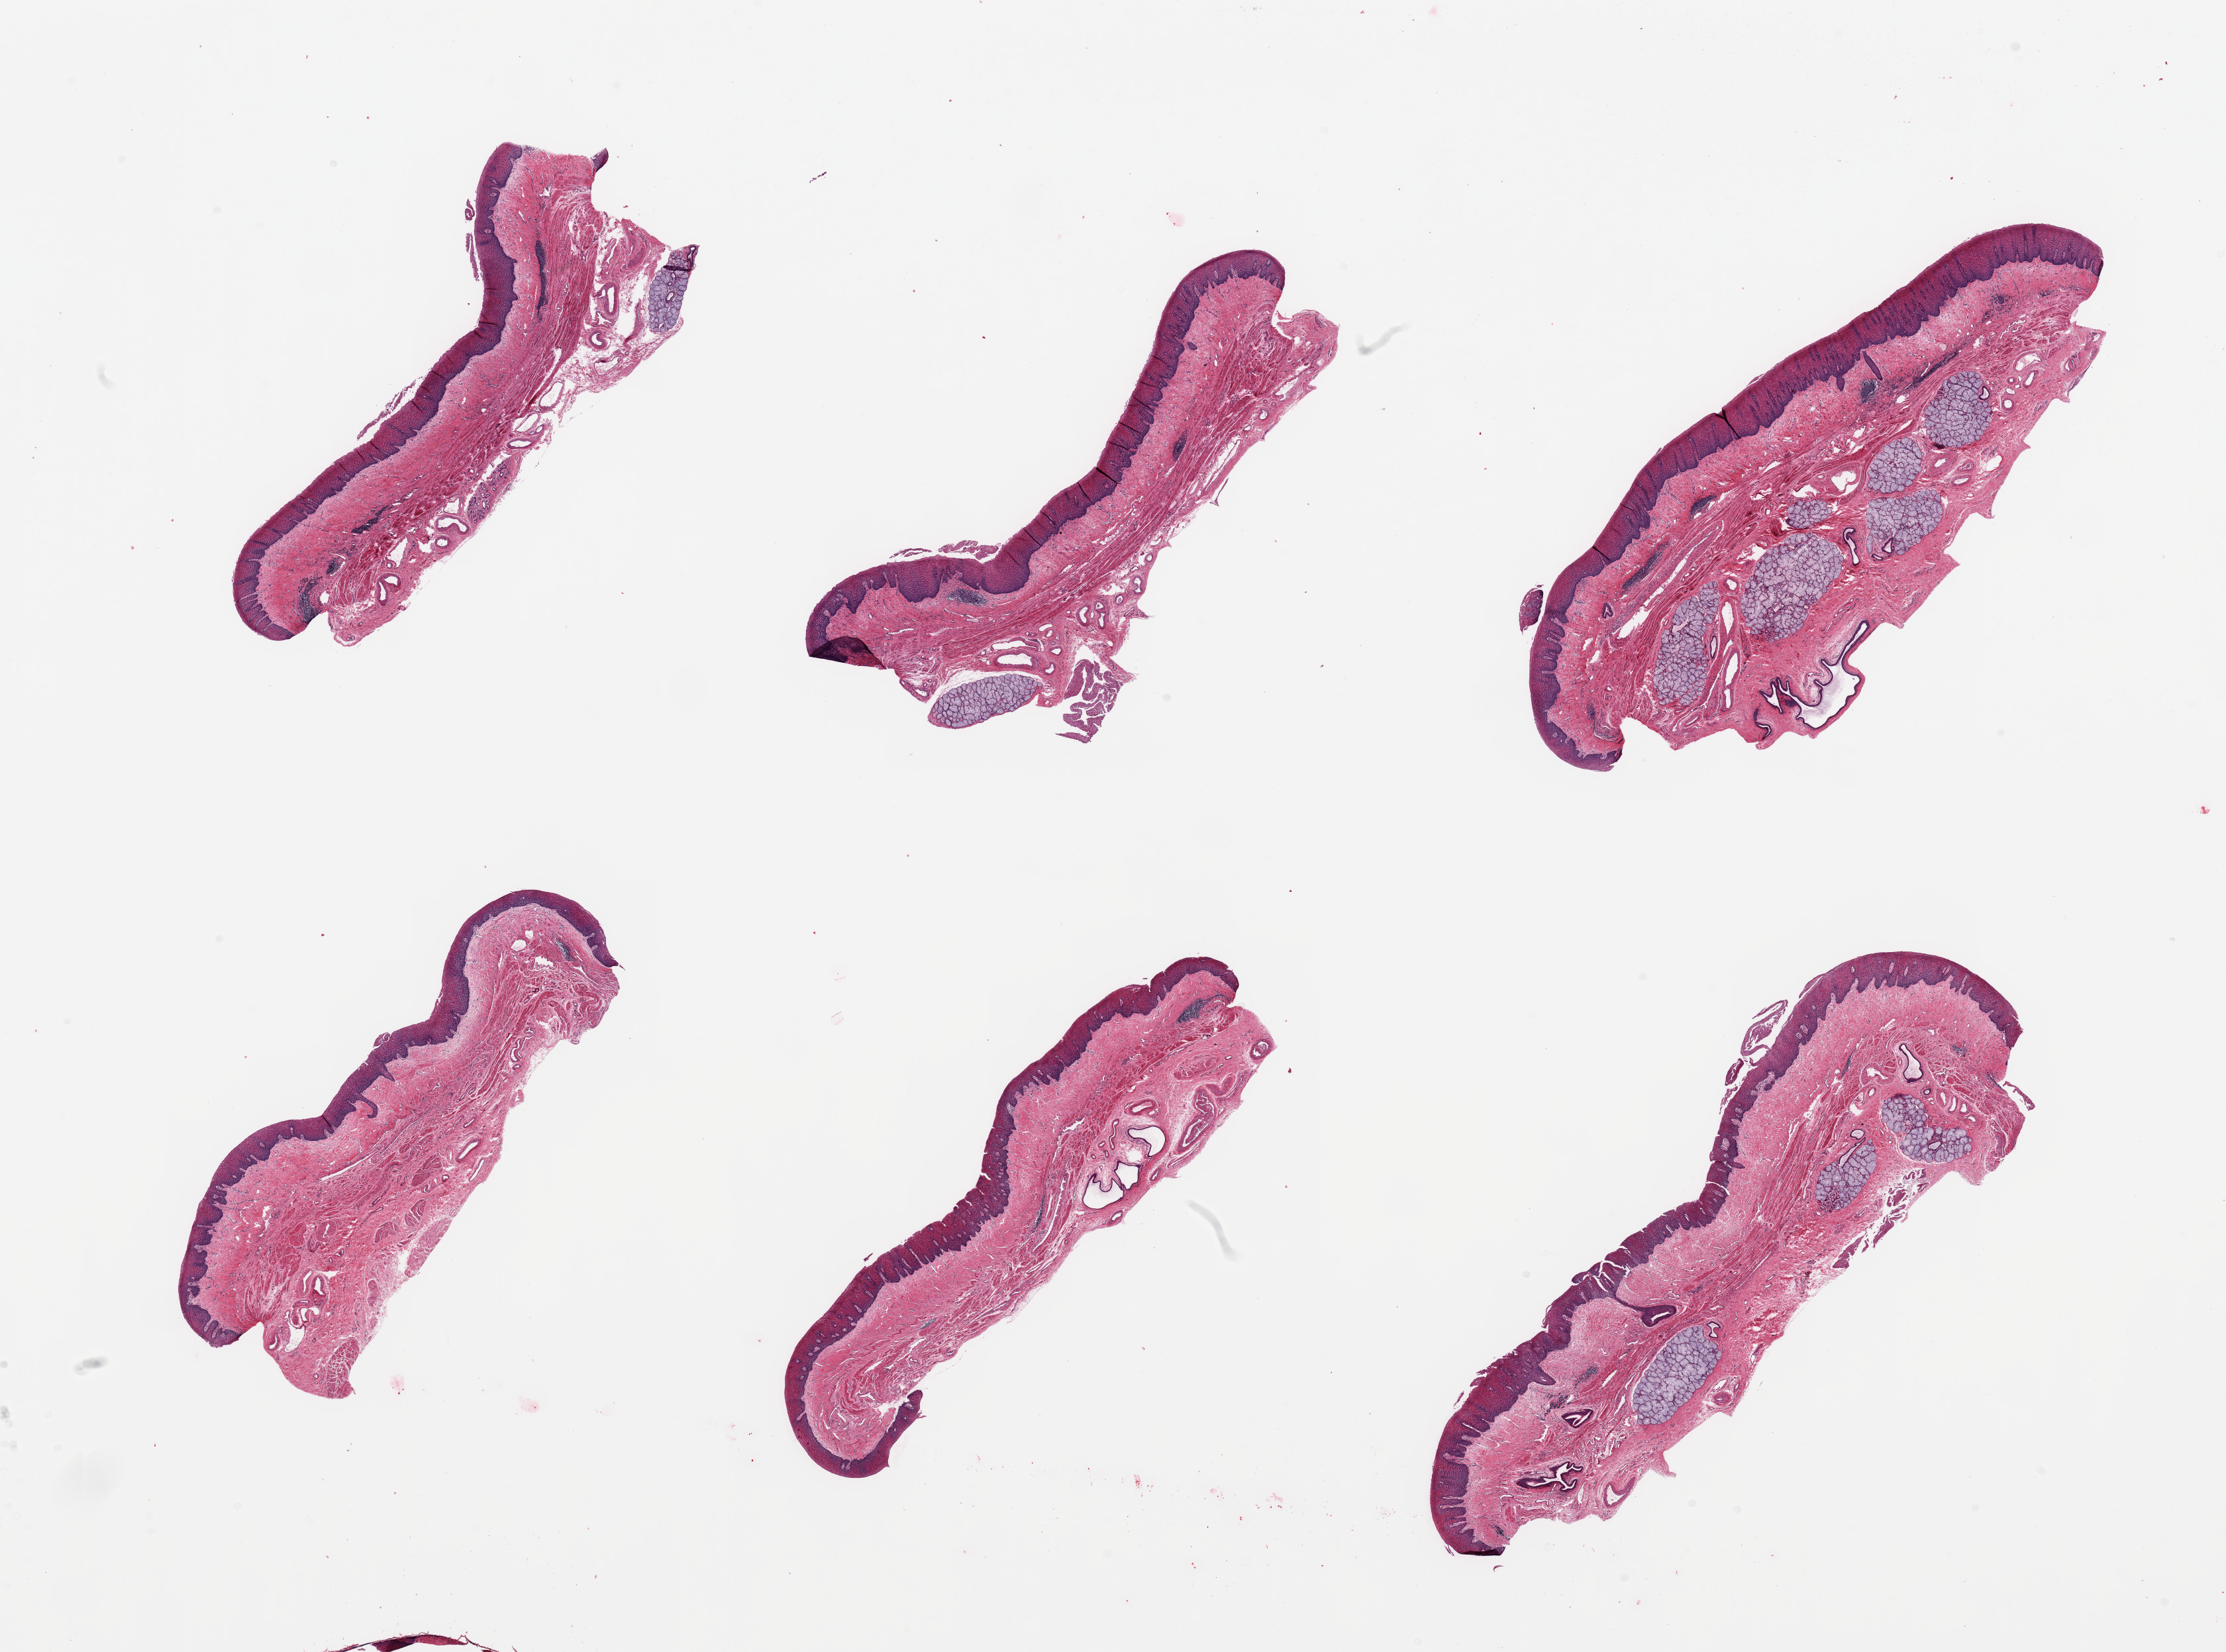
Digitized hematoxylin and eosin (H&E)-stained section — whole scanned area (about 26.6 x 19.7 mm) shown as a low-resolution overview. PAXgene-fixed, paraffin-embedded tissue. Sampled site (target tissue): esophageal mucous membrane. Donor tissue sample. Male donor.
Review note (as recorded): 6 pieces squamous mucosa up to ~0.4mm, ~20% of thickness.